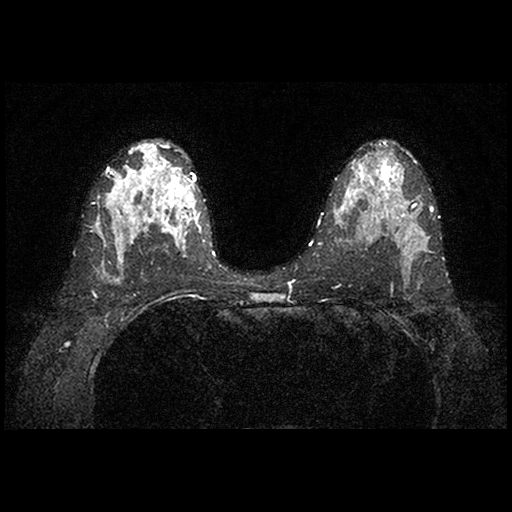
MRI of the breasts; 2 images, each one mid-volume slice chosen by position.
Image 1: fluid-sensitive (T2/STIR) axial slice, slice 43 of 84.
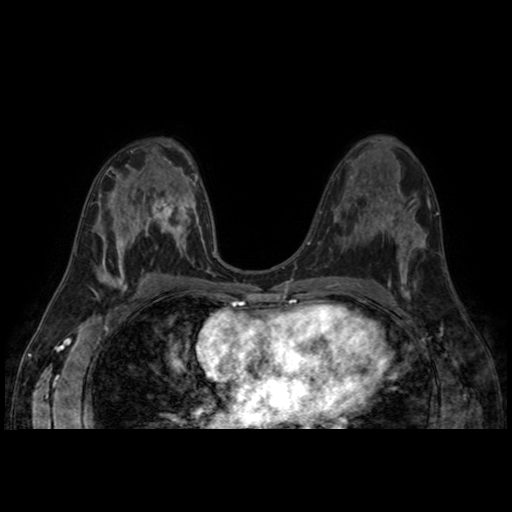
Image 2: post-contrast dynamic axial slice, series "AX BLISS_AUTO SENSE", slice 43 of 84, dynamic phase 5 of 8, 4 mm slice thickness.
MRI impression (as recorded): The breasts demonstrate moderate background enhancement. Three masses are seen within the lateral mid left breast. From anterior to
posterior, they are as follows: At 4:00, in the anterior depth, there
is a 1.1 x 0.4 x 1.4 cm oval nodule. At 4:00, in the middle depth,
there is a 2.0 x 1.2 x 1.6 cm oval mass. At 3:00 in the posterior
depth, there is a 1.2 x 1.1 x 1.2 cm round mass, which likely
corresponds to the lesion which was biopsied. All 3 masses demonstrated
a mixture of continuous, plateau, and washout enhancement kinetics with
rapid initial uptake of contrast. The total volume of tissue occupied
by the masses measures 6 cm AP x 3 cm transverse x 3 cm craniocaudal.
The most posterior mass located 1.5 cm from the pectoralis muscle.
There is no evidence of chest wall invasion. No enlarged lymph nodes are identified. No skin thickening or nipple retraction is seen. No suspicious masses or suspicious foci of contrast enhancement are seen within the right breast.
IMPRESSION:
1. Three masses within the lateral left breast. The 1 cm mass at 3:00
in the posterior depth most likely corresponds to the biopsy-proven
breast cancer. The 2 other masses demonstrates similar enhancement
kinetics and are highly suspicious for malignancy.
2. No MR evidence of invasive malignancy within the right breast; BI-RADS 6.
Patient-level pathology facts (from the clinical record, not from the images): pathology diagnosis: INVASIVE DUCTAL CARCINOMA, MODIFIED SCARFF-BLOOM-RICHARDSON GRADE-I/III. A LESS THAN 5% INTRADUCTAL CARCINOMA COMPONENT, NUCLEAR GRADE-II/III, IS ALSO PRESENT. (left breast); receptor status (as recorded): ER pos (strong), PR pos (strong), HER2 pos; Ki-67 (as recorded): intermed prolif; pathology report notes: mastectomy; INVASIVE DUCTAL CARCINOMA, MODIFIED SCARFF-BLOOM-RICHARDSON GRADE-I/III. A LESS THAN 5% INTRADUCTAL CARCINOMA COMPONENT, NUCLEAR GRADE-II/III, IS ALSO PRESENT; clinical background (as recorded): early 40s with left breast cancer. LMP unknown.